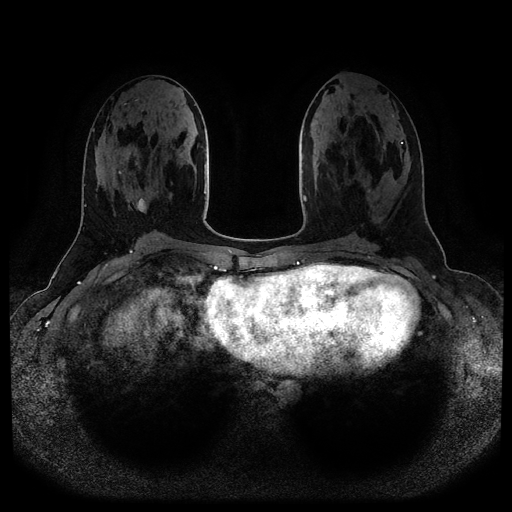
Breast MRI (dynamic contrast-enhanced, multi-phase), one axial slice; position 44 of 116 along the scan axis; dynamic contrast-enhanced series, time point 2 of 5 at this slice position (early post-contrast); 1.5 T; TE 2.6 ms, TR 5.2 ms; 2 mm slice thickness; 512 × 512 image matrix, field of view 380 × 380 mm. Patient: female, 25 years.
Outlined on this slice (semi-automatic segmentation, software-assisted and operator-edited):
- breast lesion (labelled benign in the annotation): bounding box (x1, y1, x2, y2) in pixels: (136, 198, 146, 213)